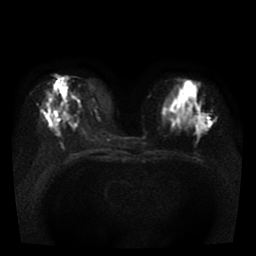
Breast MRI, one axial slice. Position 12 of 38 along the scan axis. Diffusion-weighted series; image 2 of 4 stored at this slice position (different b-values; order by instance number). 1.5 T. 5 mm slice thickness. 256 × 256 image matrix, field of view 330 × 330 mm. Female patient.
Outlined on this slice (outlined manually by an expert reader):
- tumour on diffusion-weighted imaging: bounding box <196,111,212,129> (left, top, right, bottom; pixels)